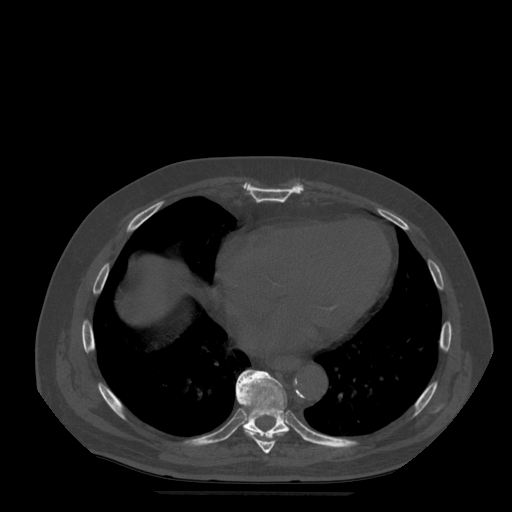
CT including the spine, one axial slice; slice 301 of 522 in the series (ordered by position); bone window (W 1800 / L 400 HU); 1.25 mm slice thickness; 512 × 512 image matrix. Patient age 72 years. From the clinical record (not read from this slice): primary cancer: prostate.
Annotated regions visible in this slice (semi-automatic segmentation, software-assisted and operator-edited):
- T8 vertebra: bounding box (x1, y1, x2, y2) in pixels: (237, 377, 289, 454)
- T9 vertebra: (236, 370, 290, 438)